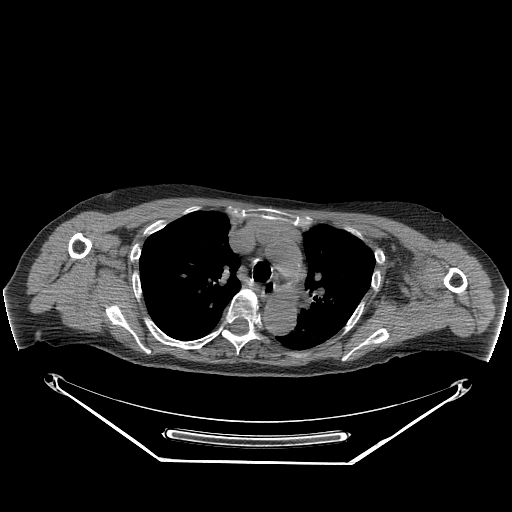
CT of an extremity soft-tissue mass (from a PET/CT study), one axial slice; position 188 of 267 along the scan axis; 140 kVp; soft-tissue window (W 400 / L 40 HU); 512 × 512 image matrix. Female patient. Case-level facts recorded for this patient, not image findings: histological type: pleiomorphic leiomyosarcoma; grade: high; site of the primary tumour: left biceps.
Annotated regions visible in this slice (expert contour drawn on MRI and transferred to this co-registered scan by the dataset authors):
- gross tumour volume including surrounding oedema: bounding box (x1, y1, x2, y2) in pixels: (415, 263, 435, 287)